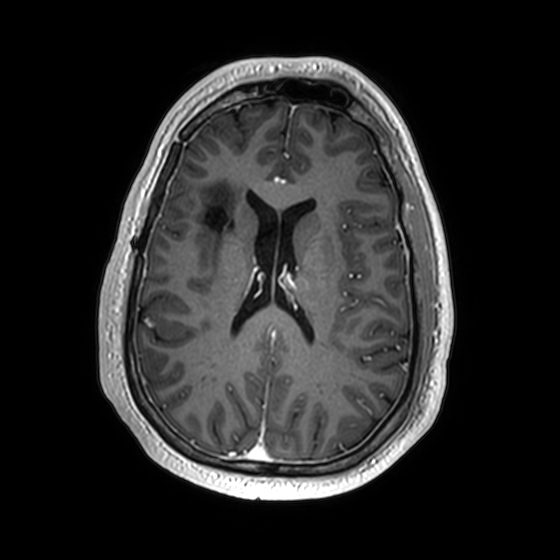
Brain MRI from a brain-tumour surgery series, one axial slice. Slice 74 of 174 in the series (ordered by position). T1-weighted post-contrast. 1 mm slice thickness. 560 × 560 image matrix. From the clinical record (not read from this slice): histopathology: Astrocytoma; WHO grade: 2; IDH mutation: yes.
Annotated regions visible in this slice (outlined manually by an expert reader):
- previous resection cavity: bounding box [x1, y1, x2, y2] px = [207, 206, 234, 231]